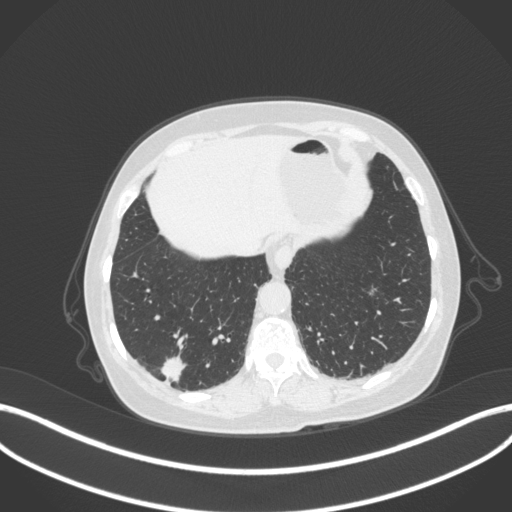
Chest CT, one axial slice. Slice 60 of 340 in the series (ordered by position). Lung window (W 1500 / L -600 HU). 1 mm slice thickness. 512 × 512 image matrix. Patient: female, 69 years. From the clinical record (not read from this slice): clinical TNM (as recorded): T1b N0 M0.
Annotated regions visible in this slice (rectangle marked by the reading radiologist):
- lung tumour (recorded histology: adenocarcinoma): bounding box [x1, y1, x2, y2] px = [156, 352, 188, 383]